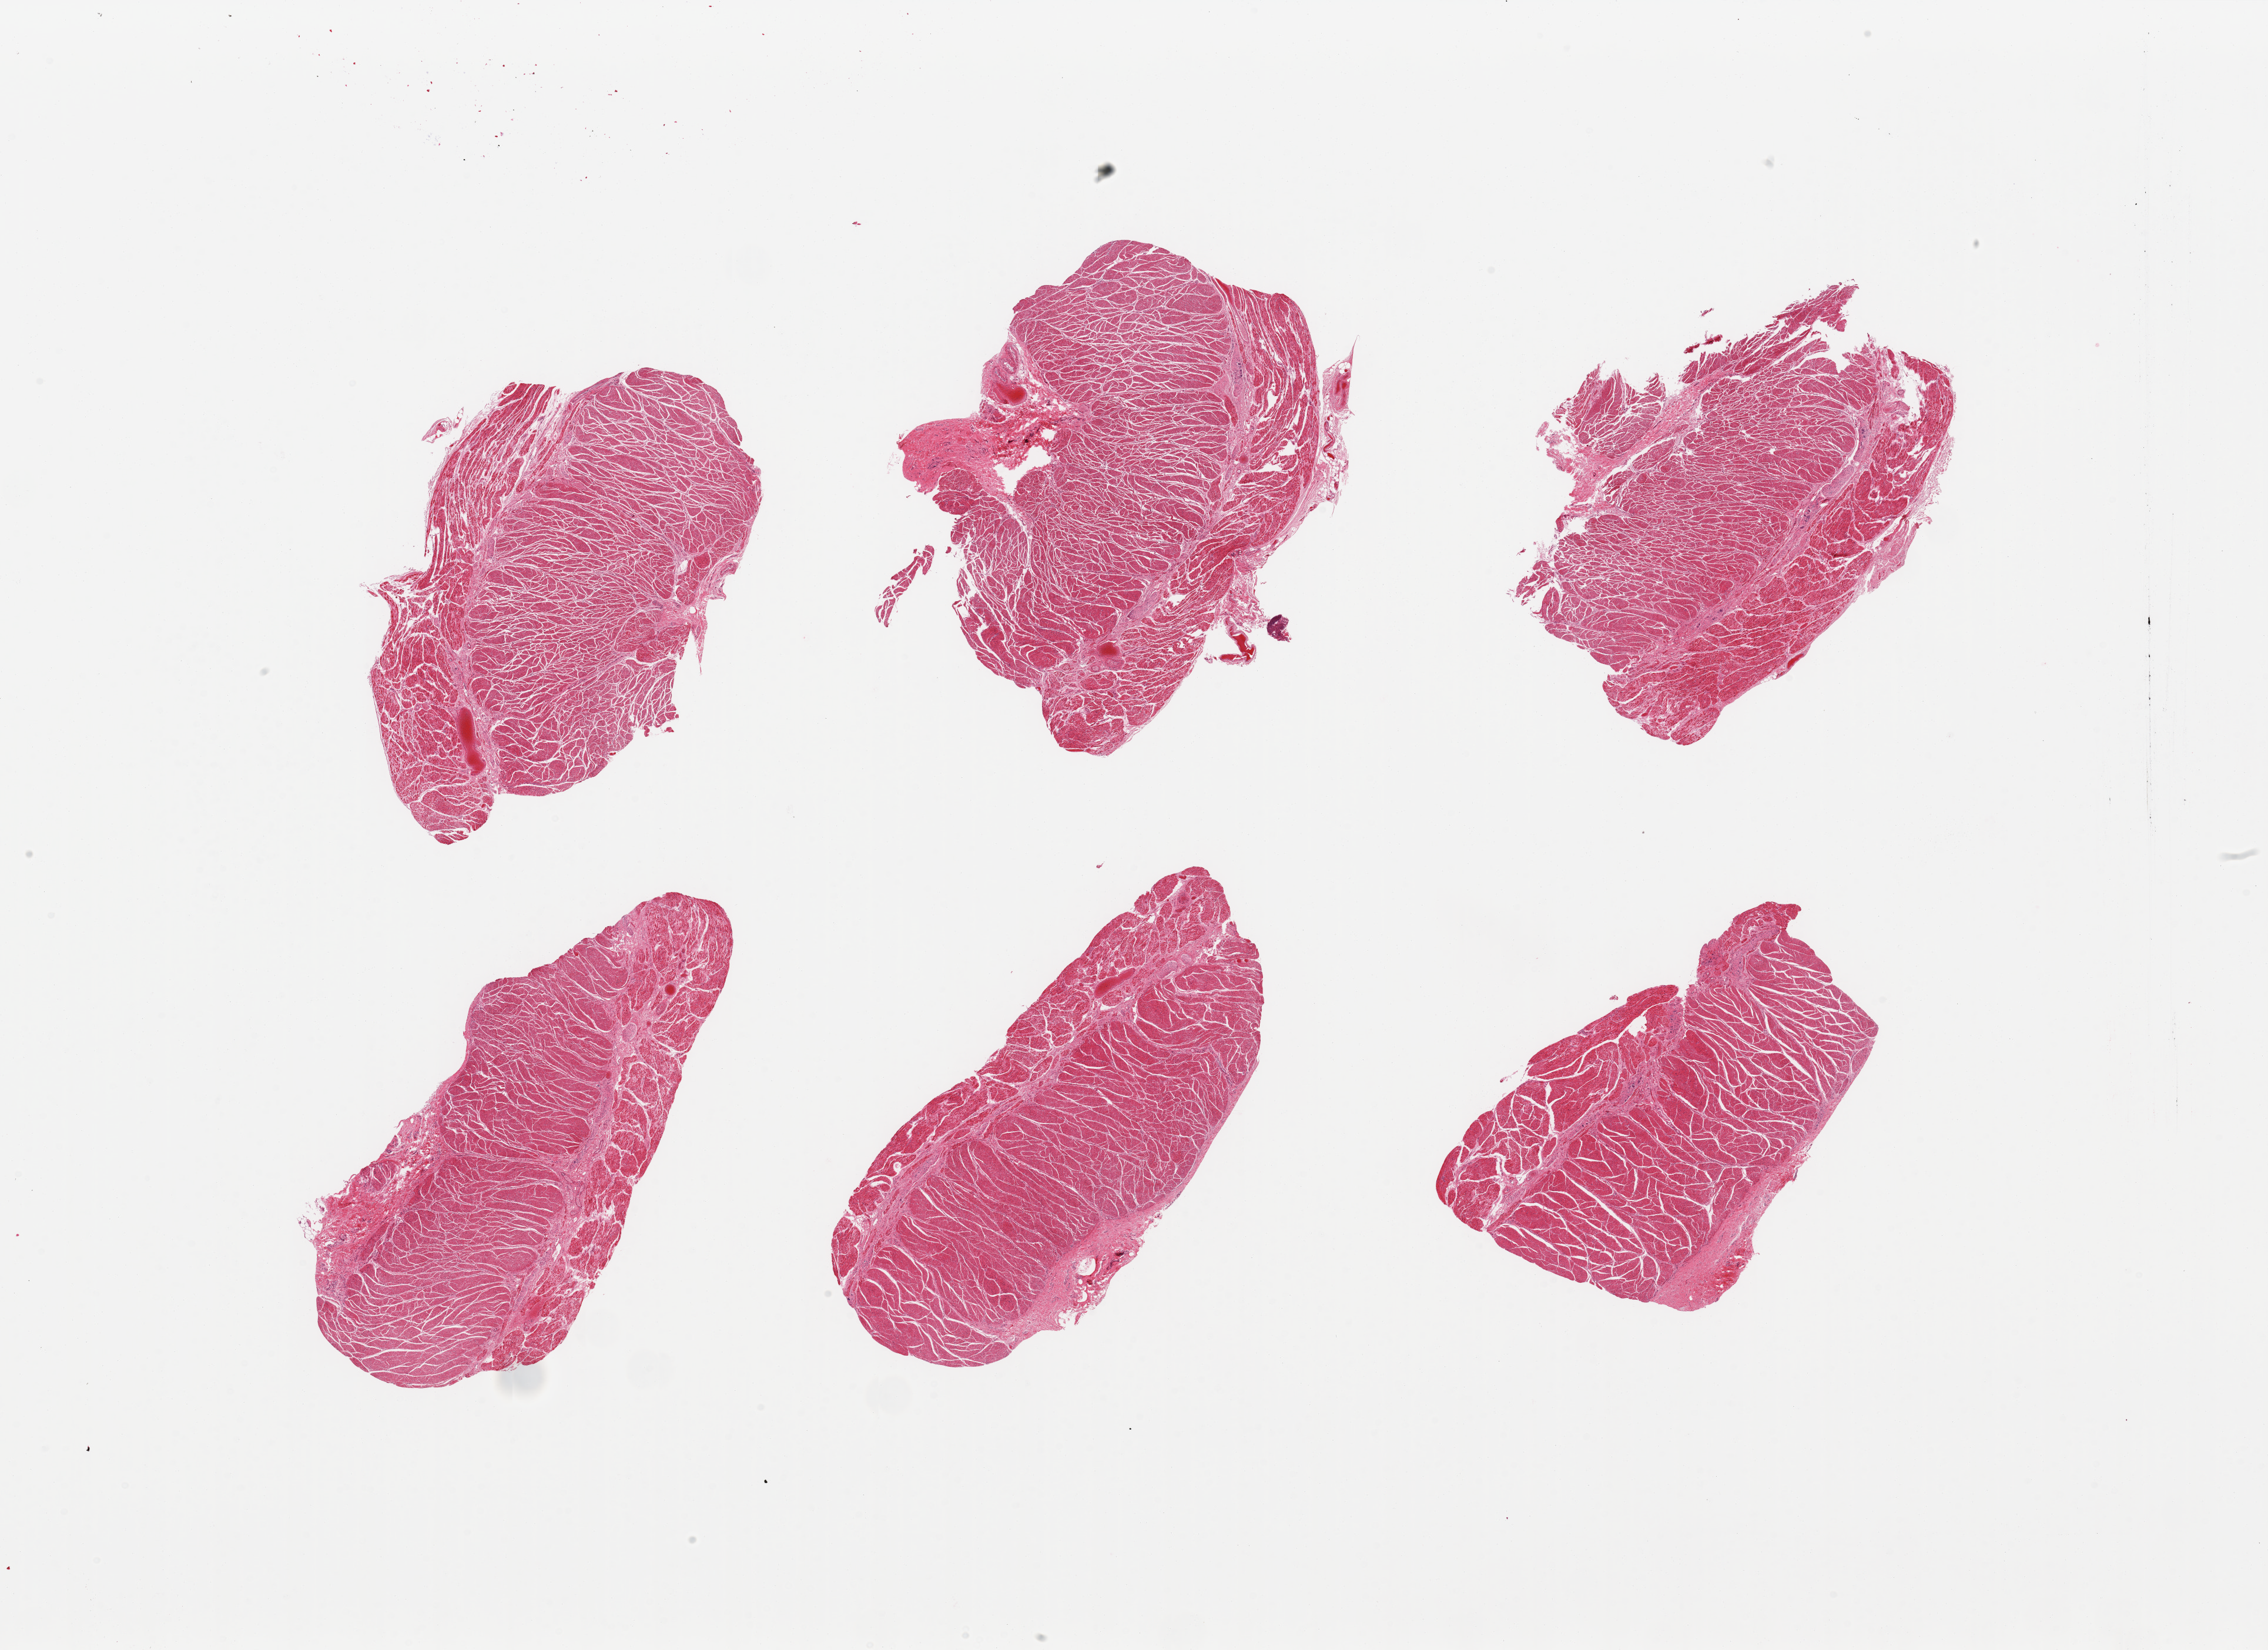
Whole-slide image, H&E stain, brightfield — shown as a low-resolution overview of the whole scanned area (about 30.5 x 22.2 mm, from a 20x scan). PAXgene-fixed, paraffin-embedded tissue. Sampled site (target tissue): gastroesophageal junction. Donor tissue sample. Donor: male.
Reviewer comment on this tissue sample: 6 pieces, confirmed target muscularis.